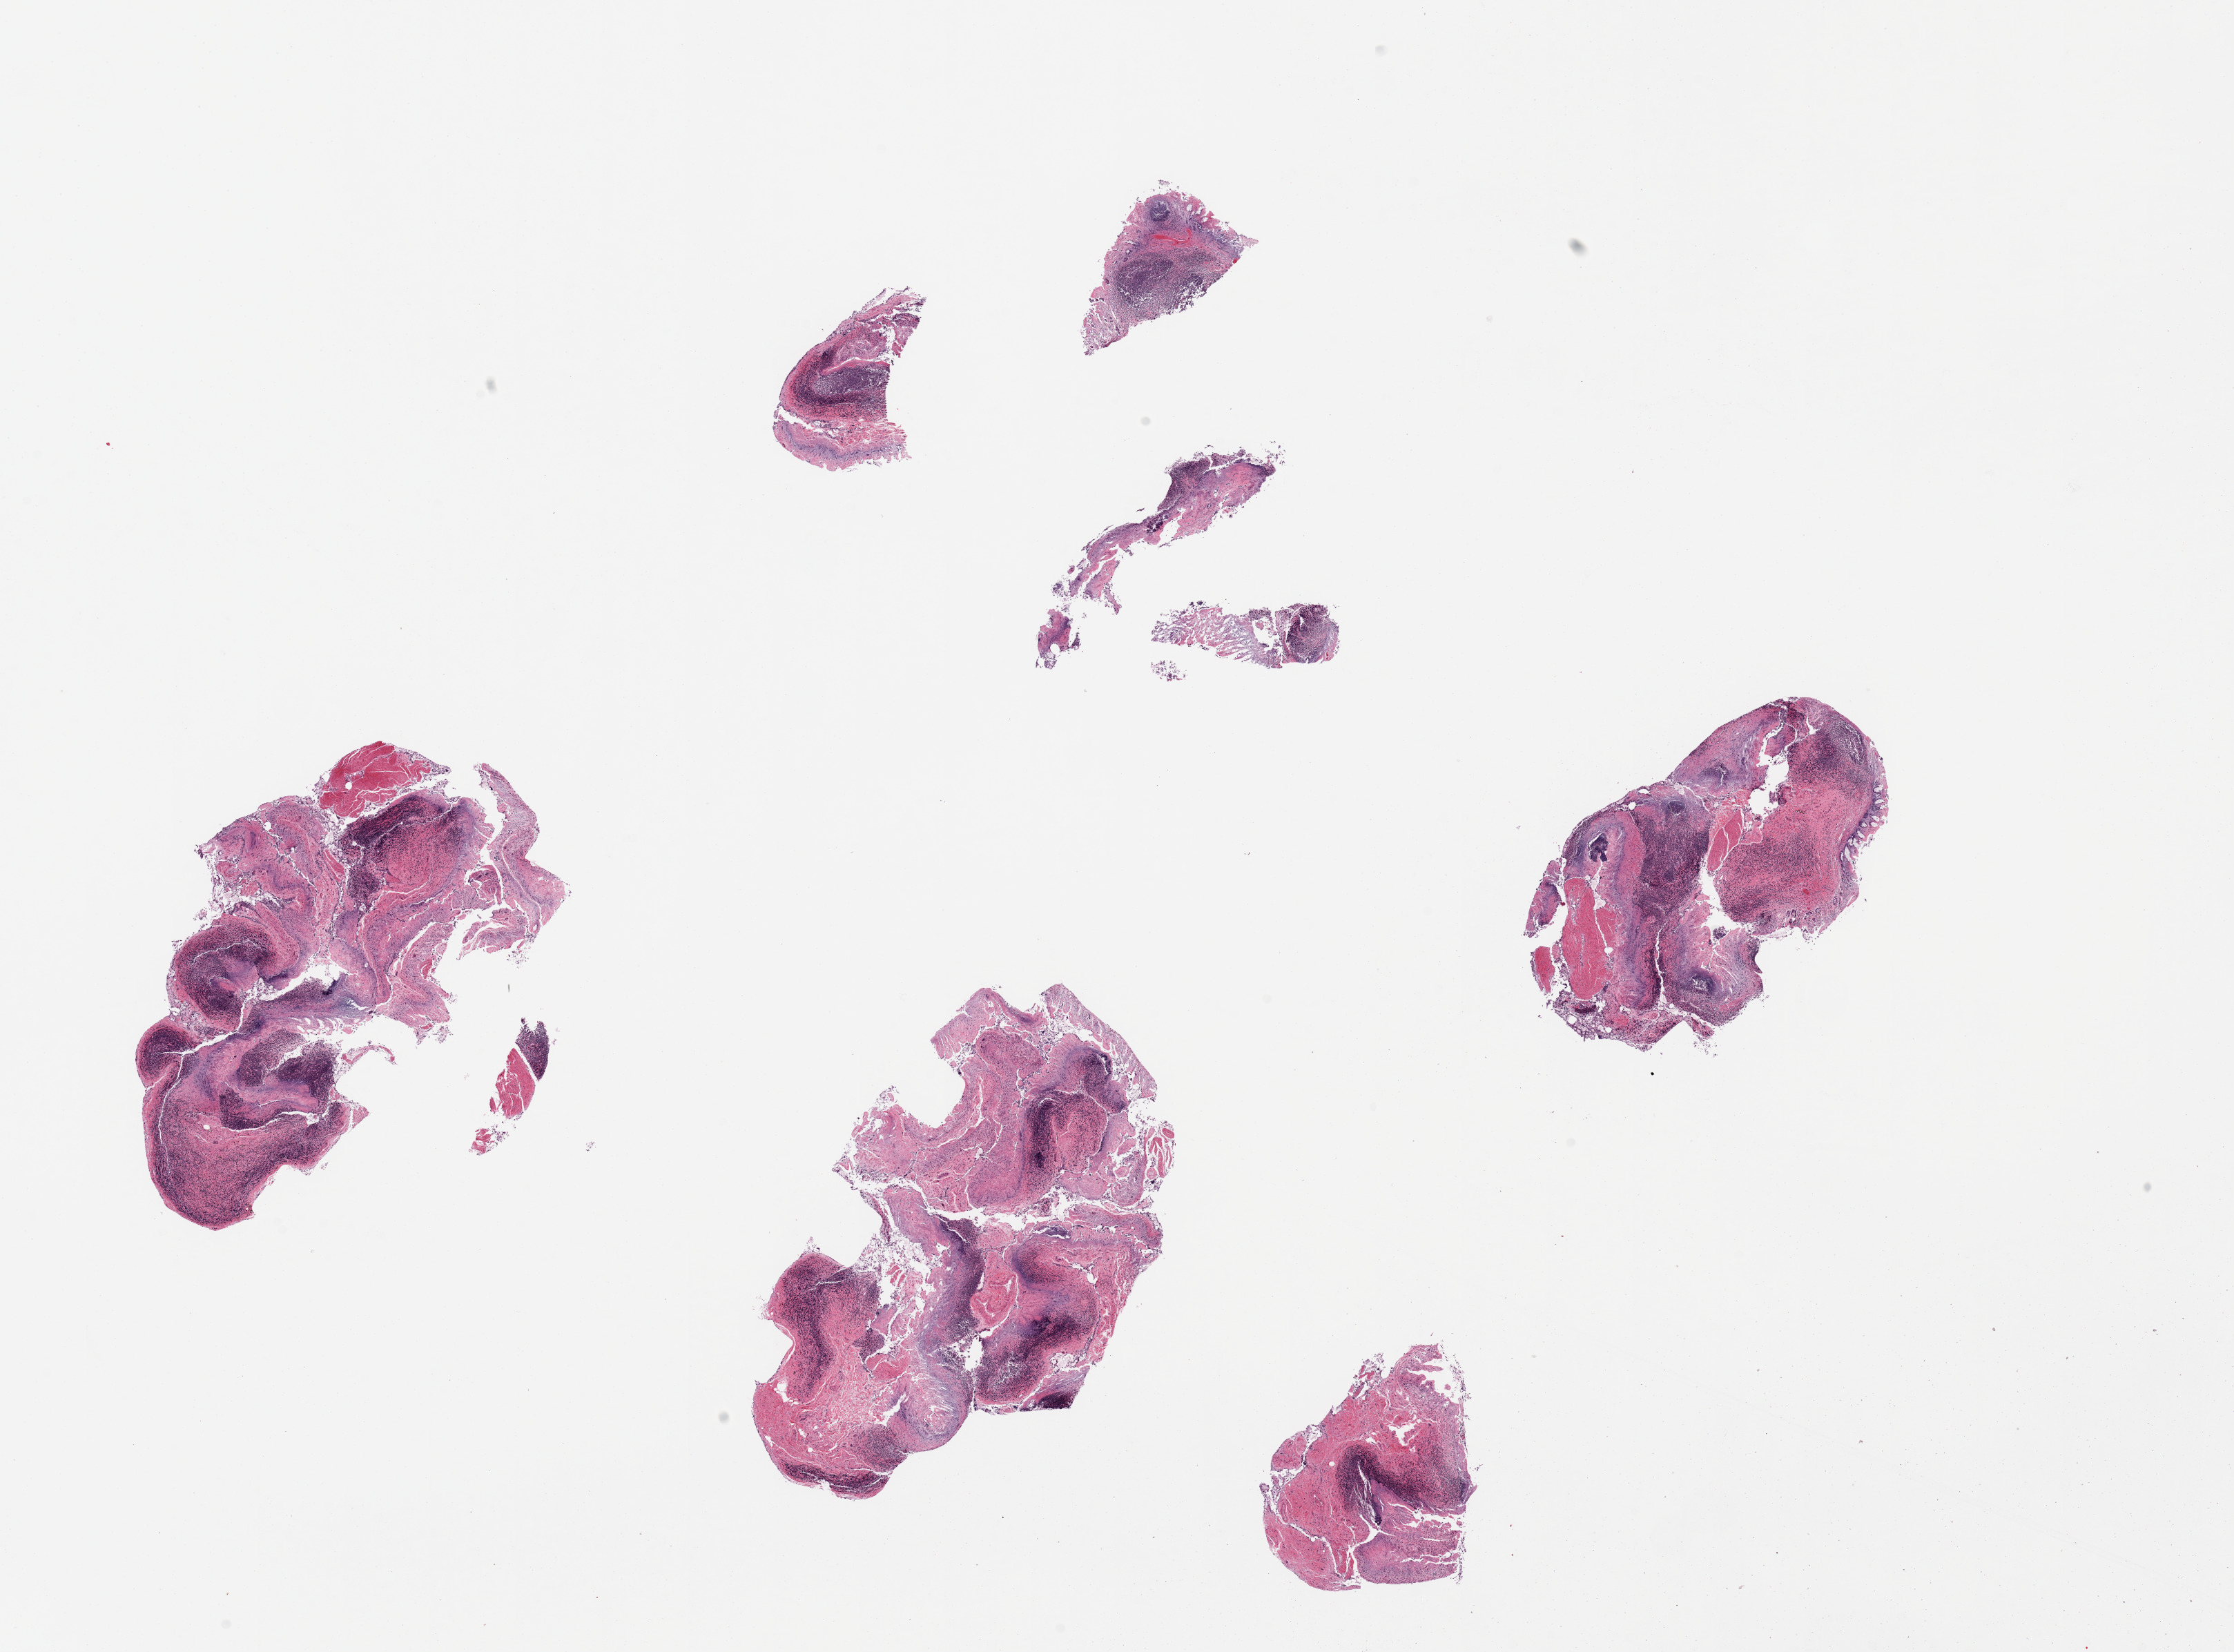
Haematoxylin and eosin whole-slide image — low-resolution overview of the scanned area, about 25.6 x 18.9 mm, PAXgene-fixed paraffin-embedded (PFPE) section, target tissue: ileum, donor tissue sample. Donor sex: female.
Pathologist's review note for this sample: 4 pieces, fragmented. Lymphoid elements ~20-30% total tissue but all badly autolyzed.